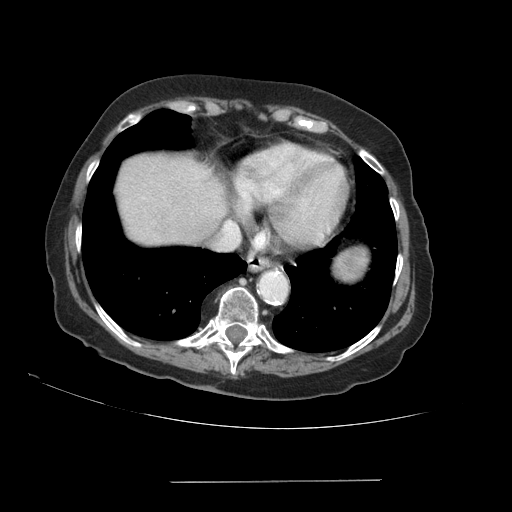
Contrast-enhanced abdominal CT (liver protocol), one axial slice; slice 80 of 89 in the series (ordered by position); reconstruction kernel STANDARD; soft-tissue window (W 400 / L 40 HU); 2.5 mm slice thickness; 512 × 512 image matrix, field of view 400 × 400 mm. Case-level facts recorded for this patient, not image findings: diagnosis: hepatocellular carcinoma (patient treated with transarterial chemoembolisation; whether this scan precedes or follows treatment is not stated here); TNM stage (as recorded): Stage-IVA; Child-Pugh class: A; tumour differentiation: poorly differentiated; tumour nodularity: uninodular.
Annotated regions visible in this slice (semi-automatic segmentation, software-assisted and operator-edited):
- liver parenchyma outside the tumour (the mass and vessels are separate outlines, so this box may not span the whole liver): bounding box <116,154,226,244> (left, top, right, bottom; pixels)